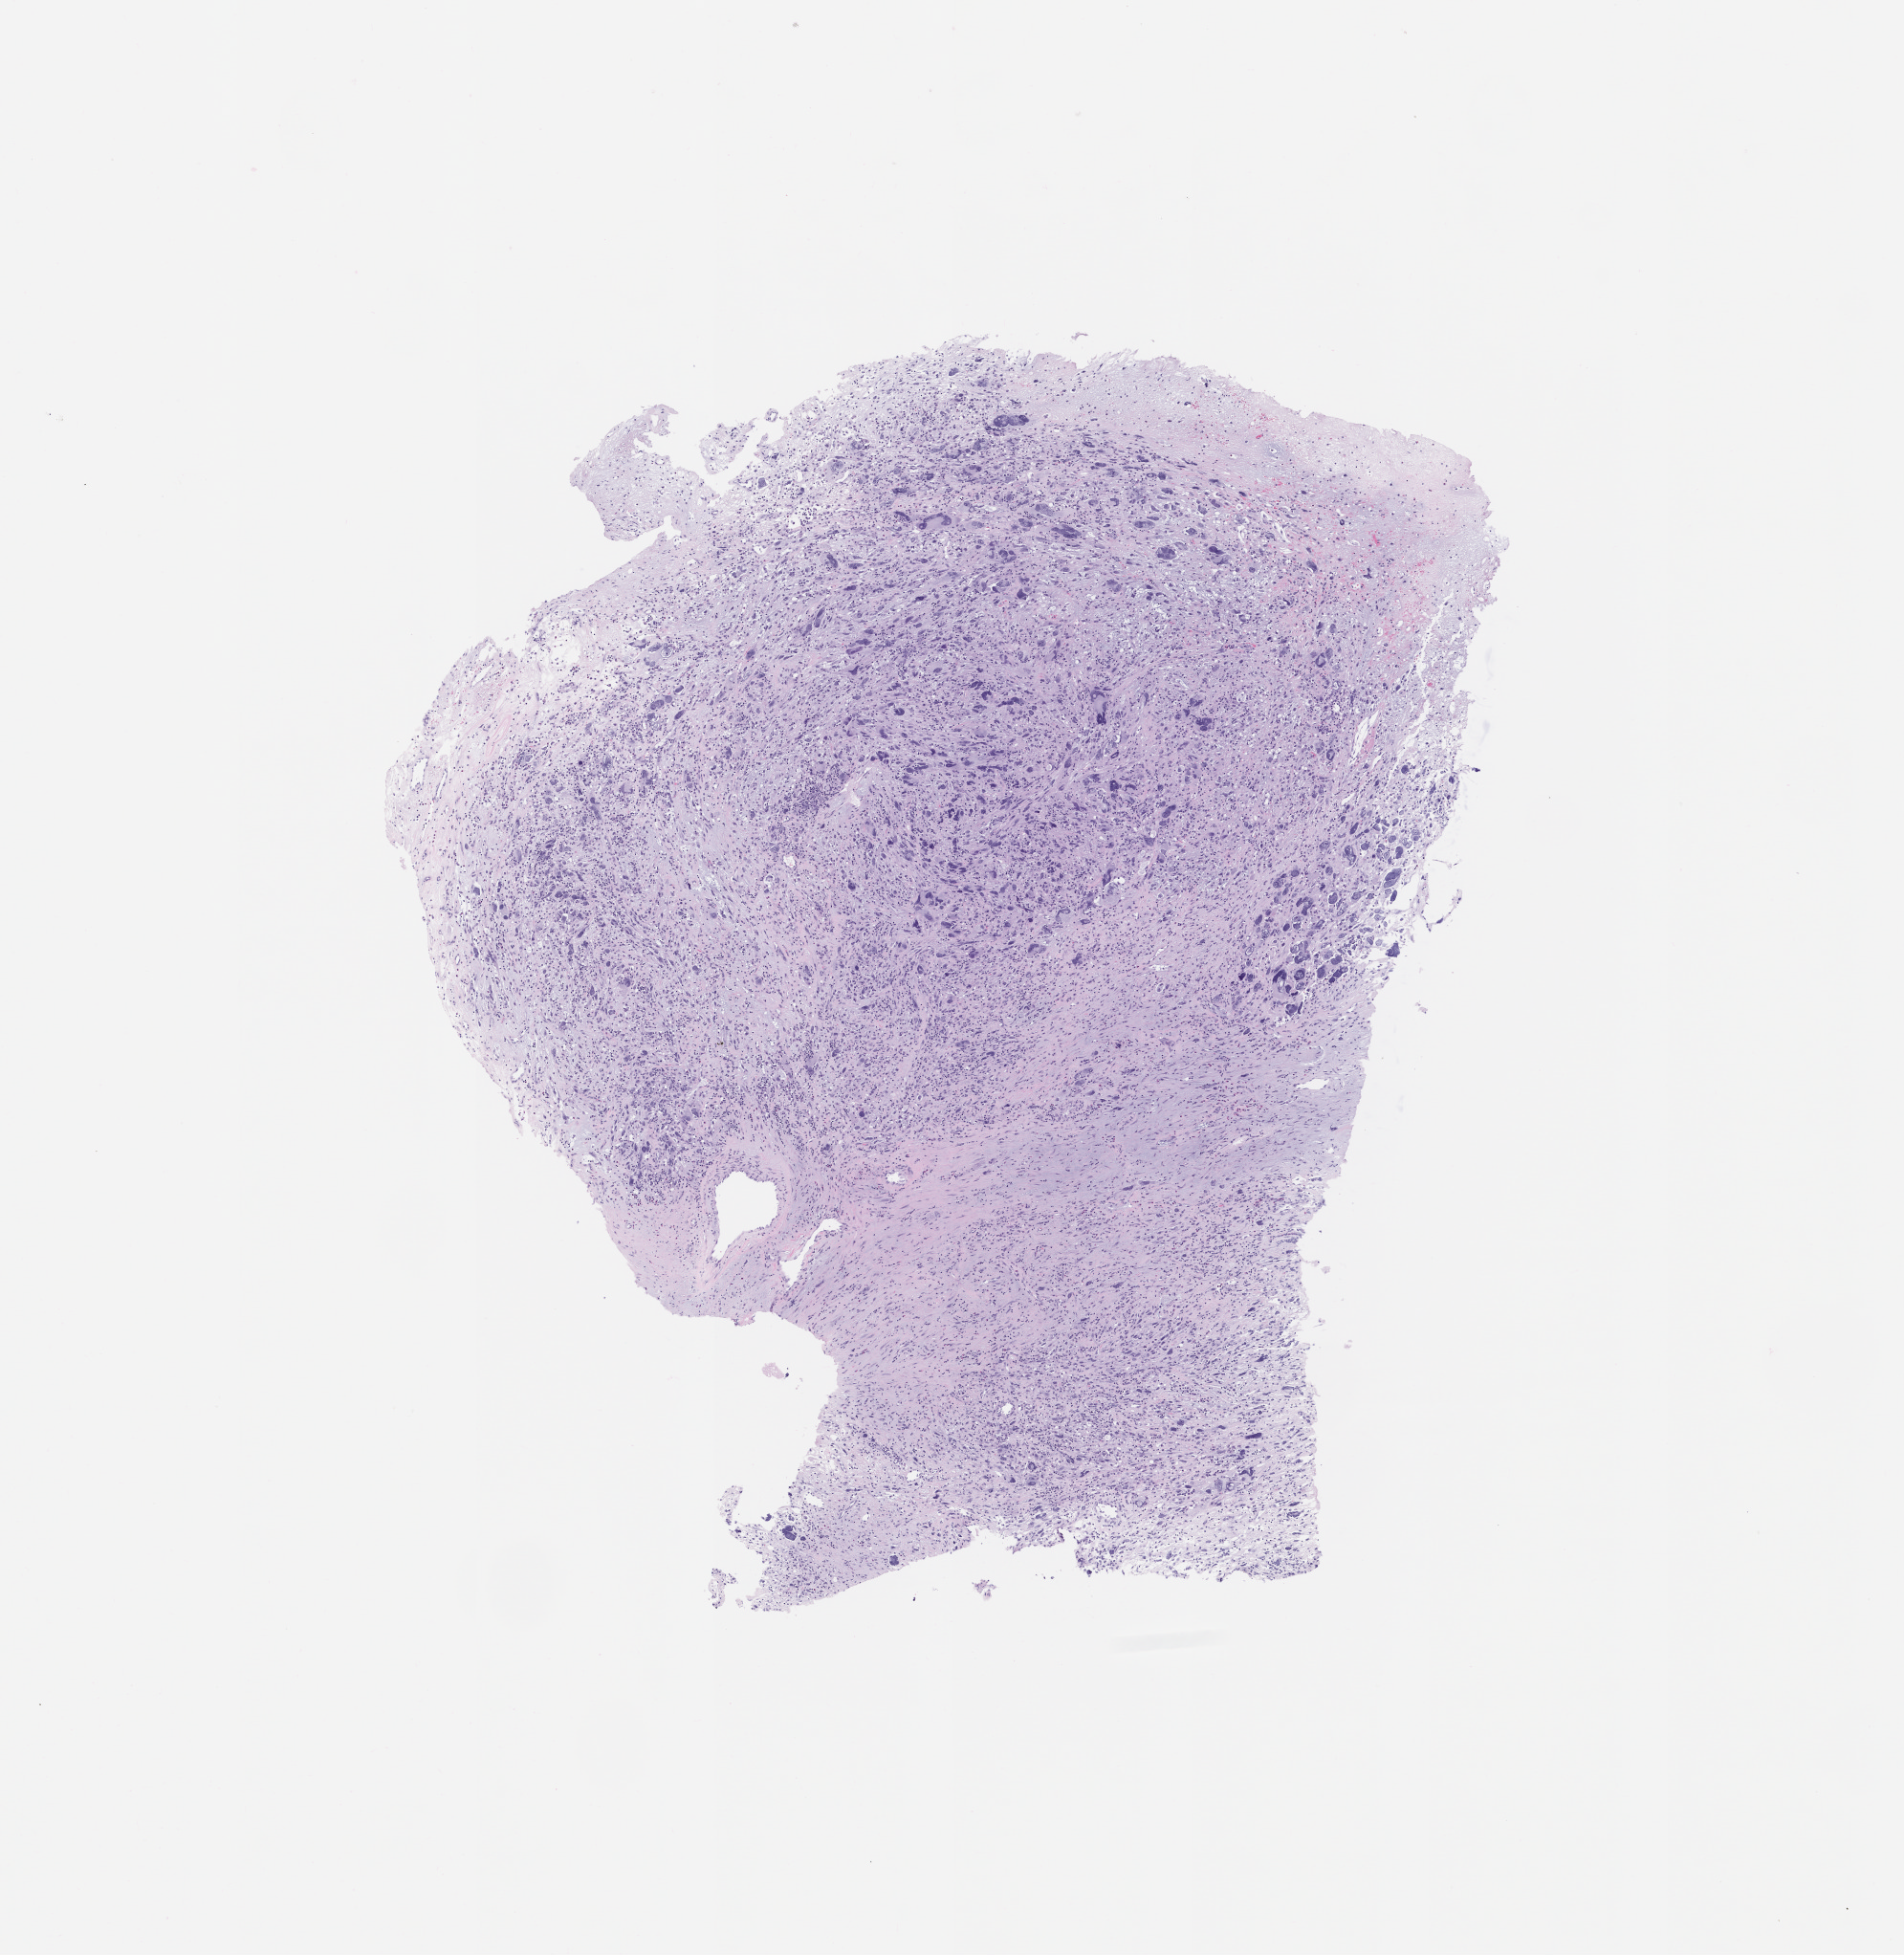
Digitized haematoxylin and eosin-stained section of the patient's (originator) tumor tissue — a low-resolution overview of the entire scanned area, about 8.0 x 8.2 mm. FFPE section. Originating tumor site category: musculoskeletal. Patient female; 43 years old.
Diagnosis: Leiomyosarcoma.